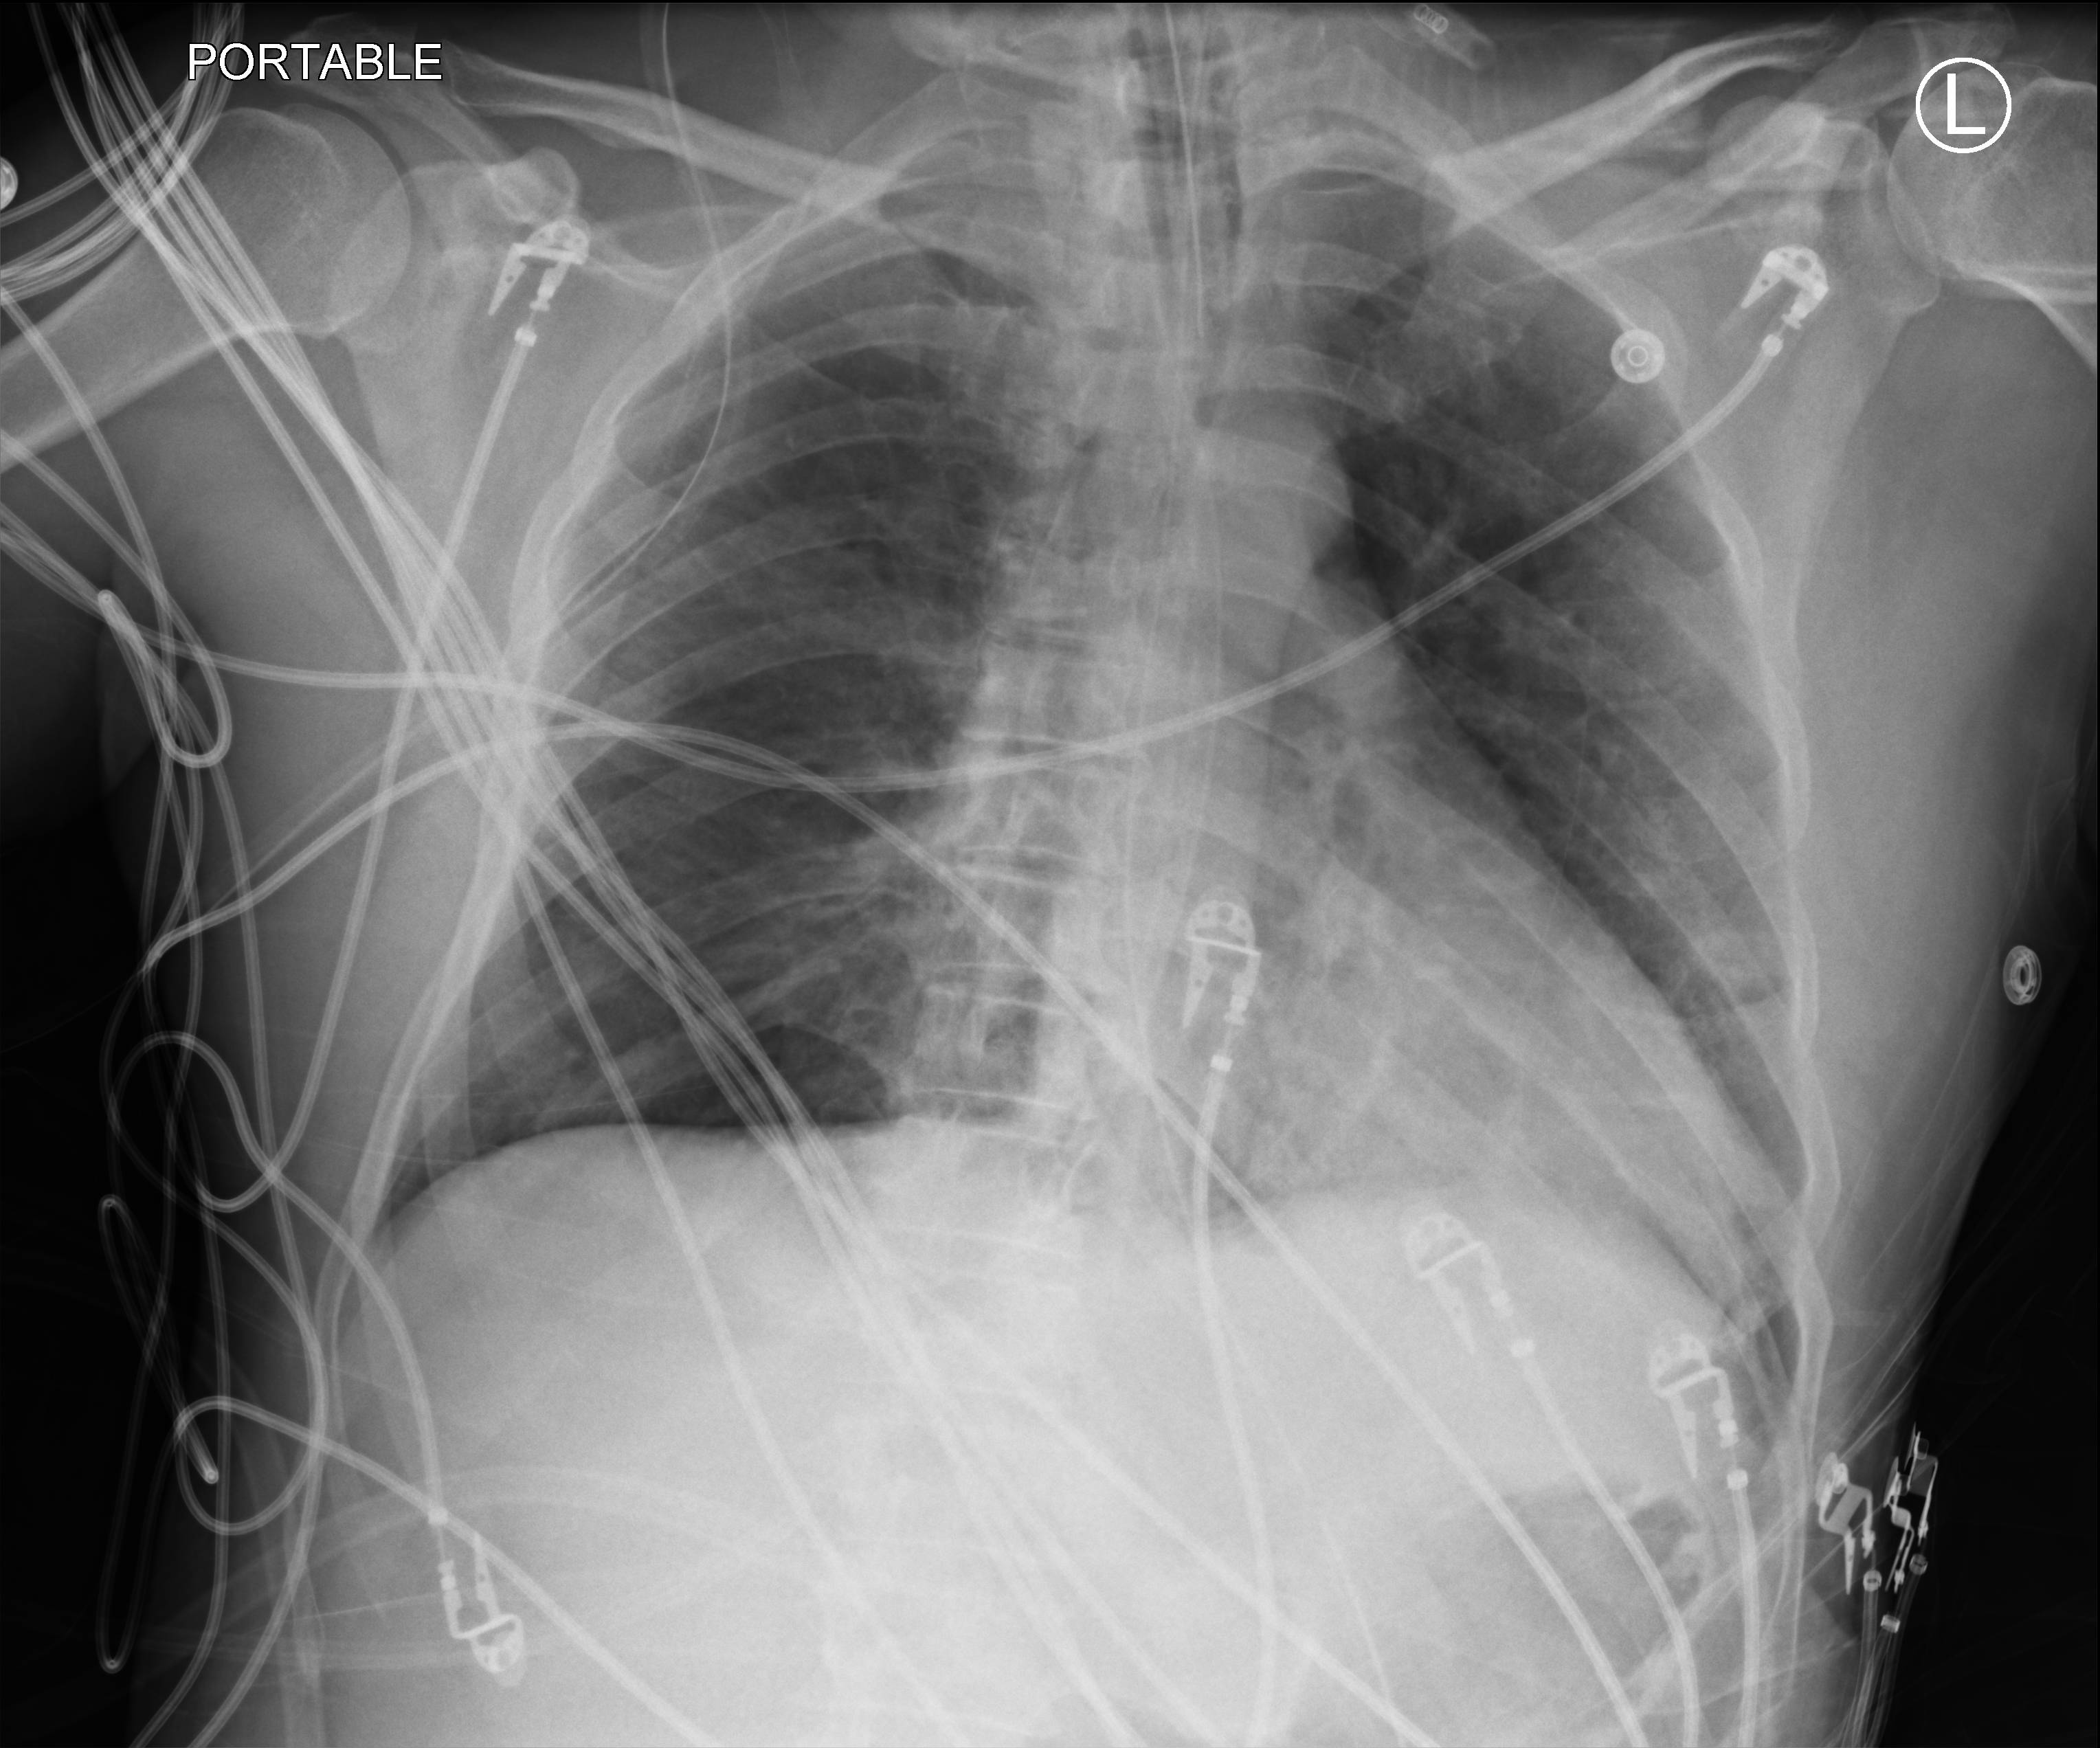
Chest X-ray (portable), anteroposterior (AP) projection. Patient hospitalised with COVID-19; male, aged 18–59 years.
From the hospital-stay record, not from the radiograph (when in the stay this image was taken is not recorded): admitted to intensive care during this hospital stay: yes.